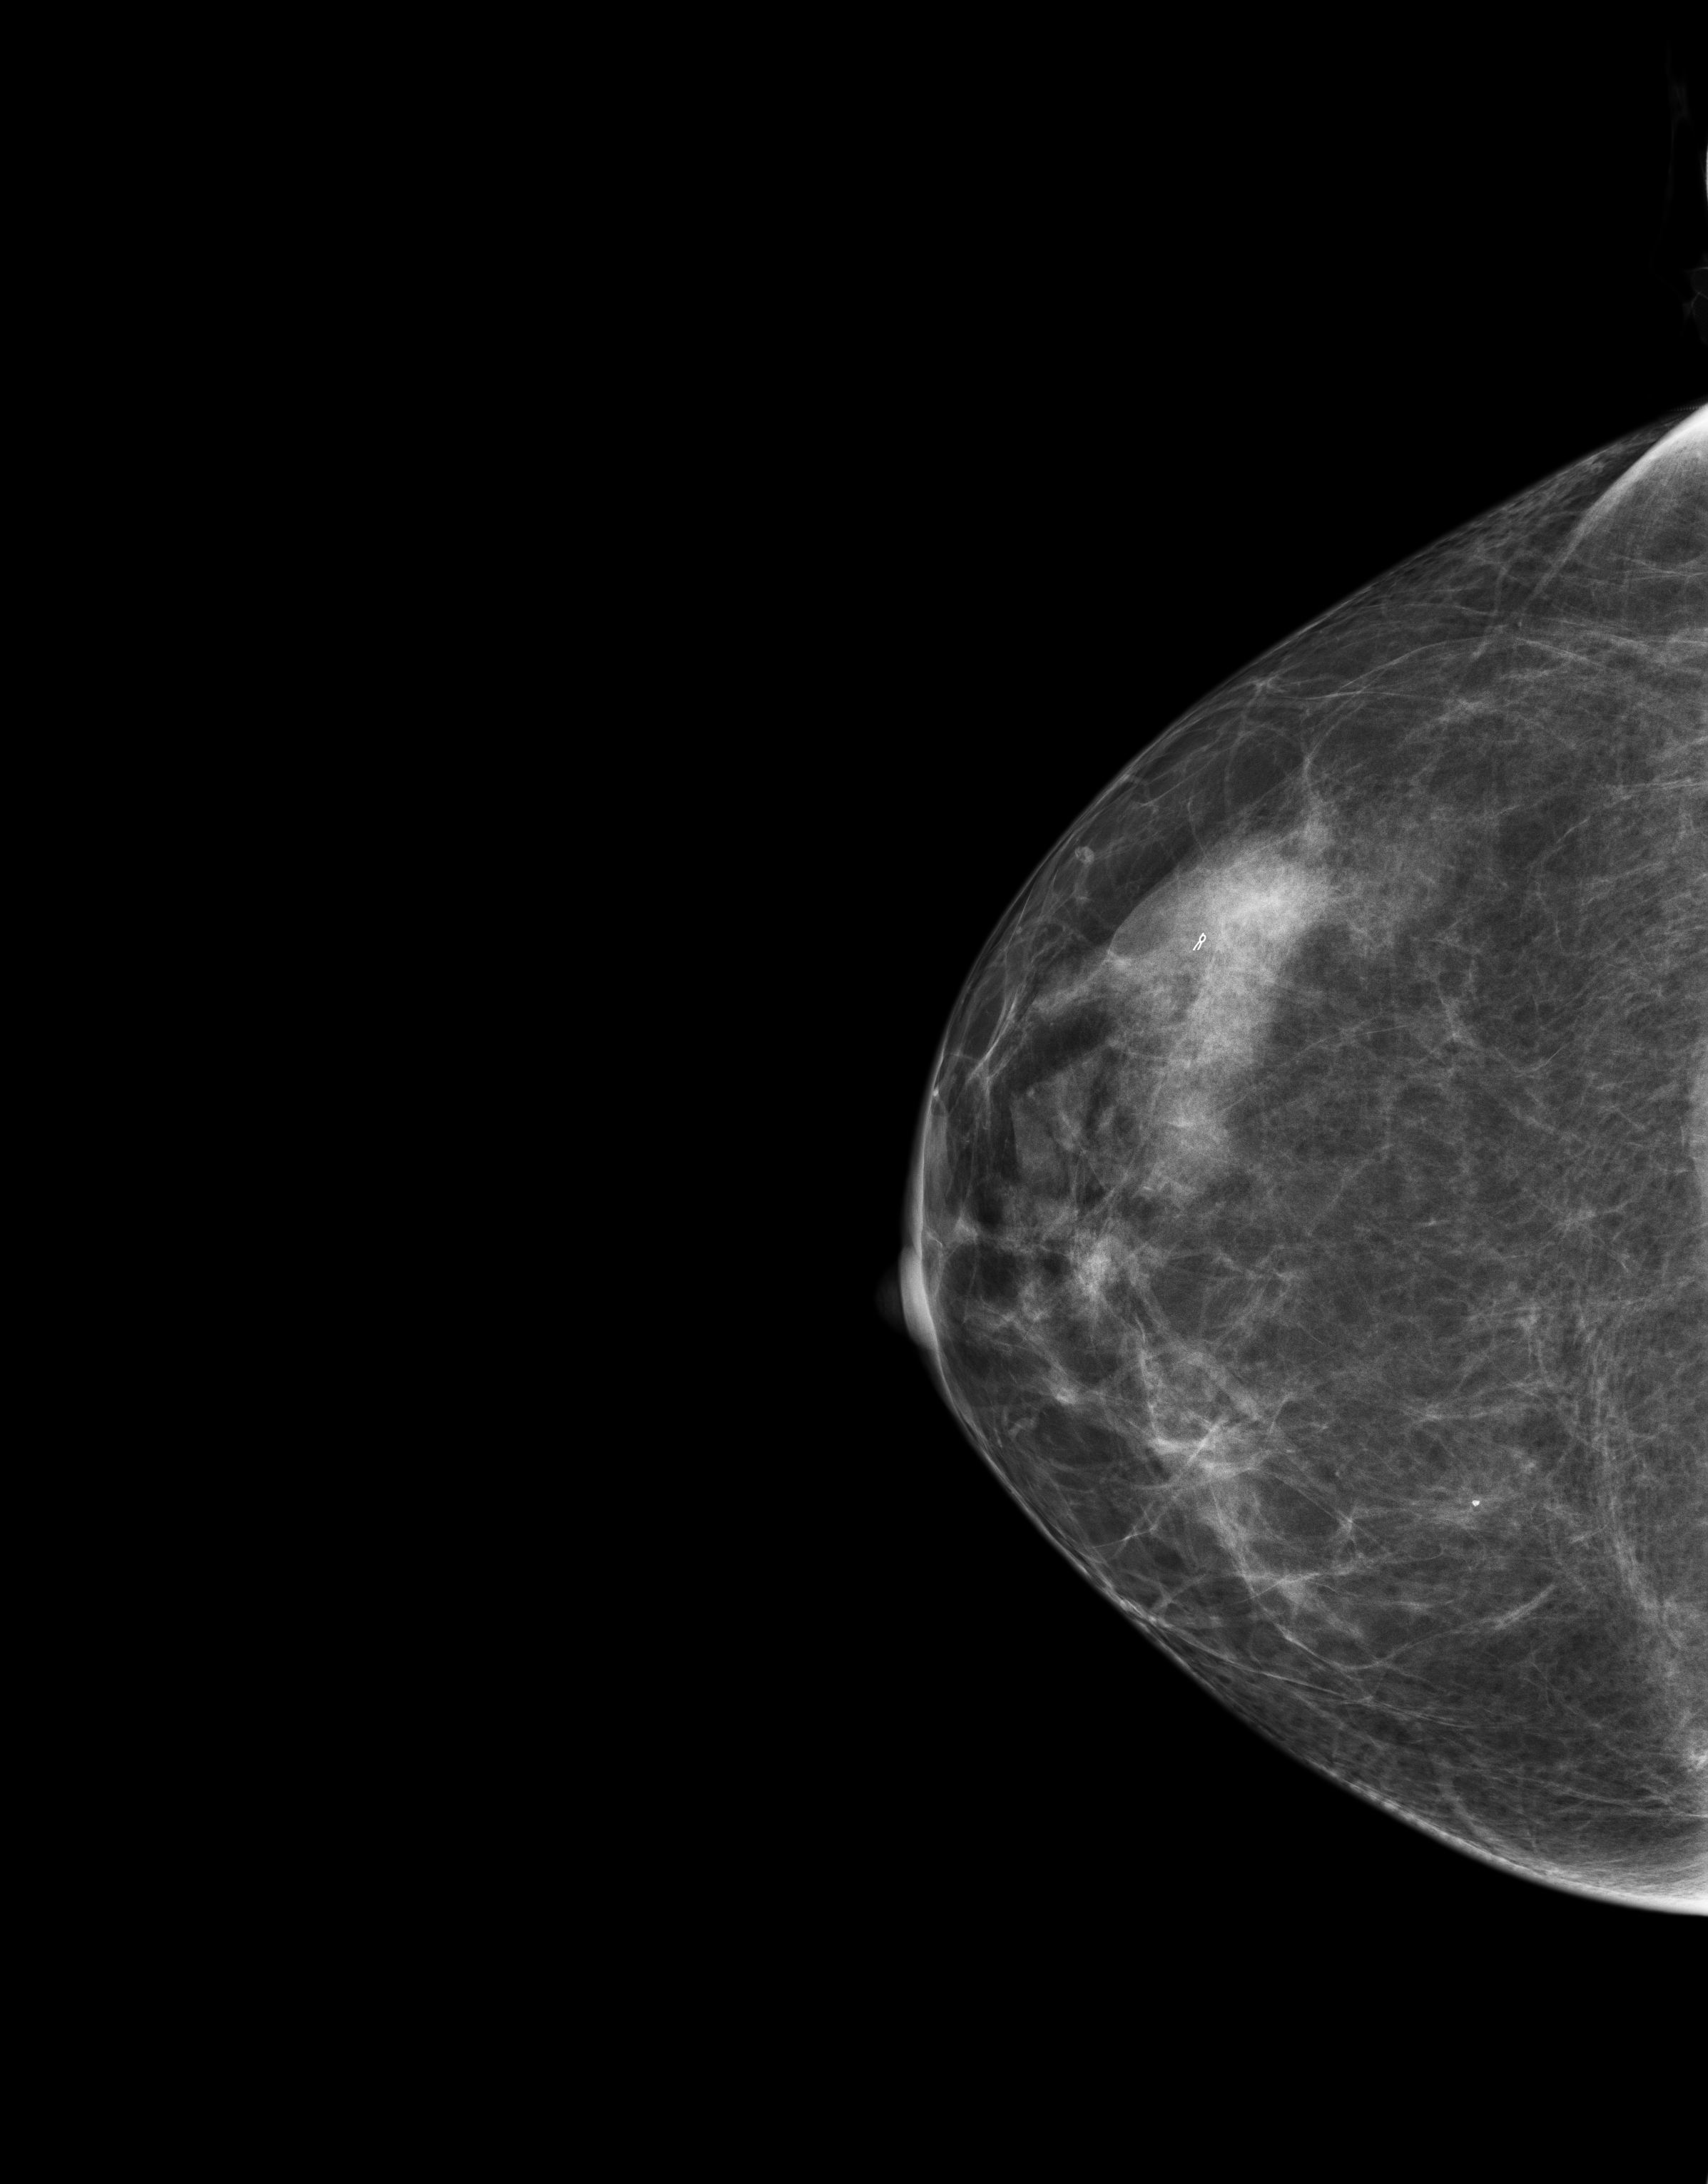
Full-field digital mammogram (FFDM), right breast, CC view, screening examination. Female patient, age 48 years.
Breast density at the screening exam (both breasts): heterogeneously dense (BI-RADS density category c).